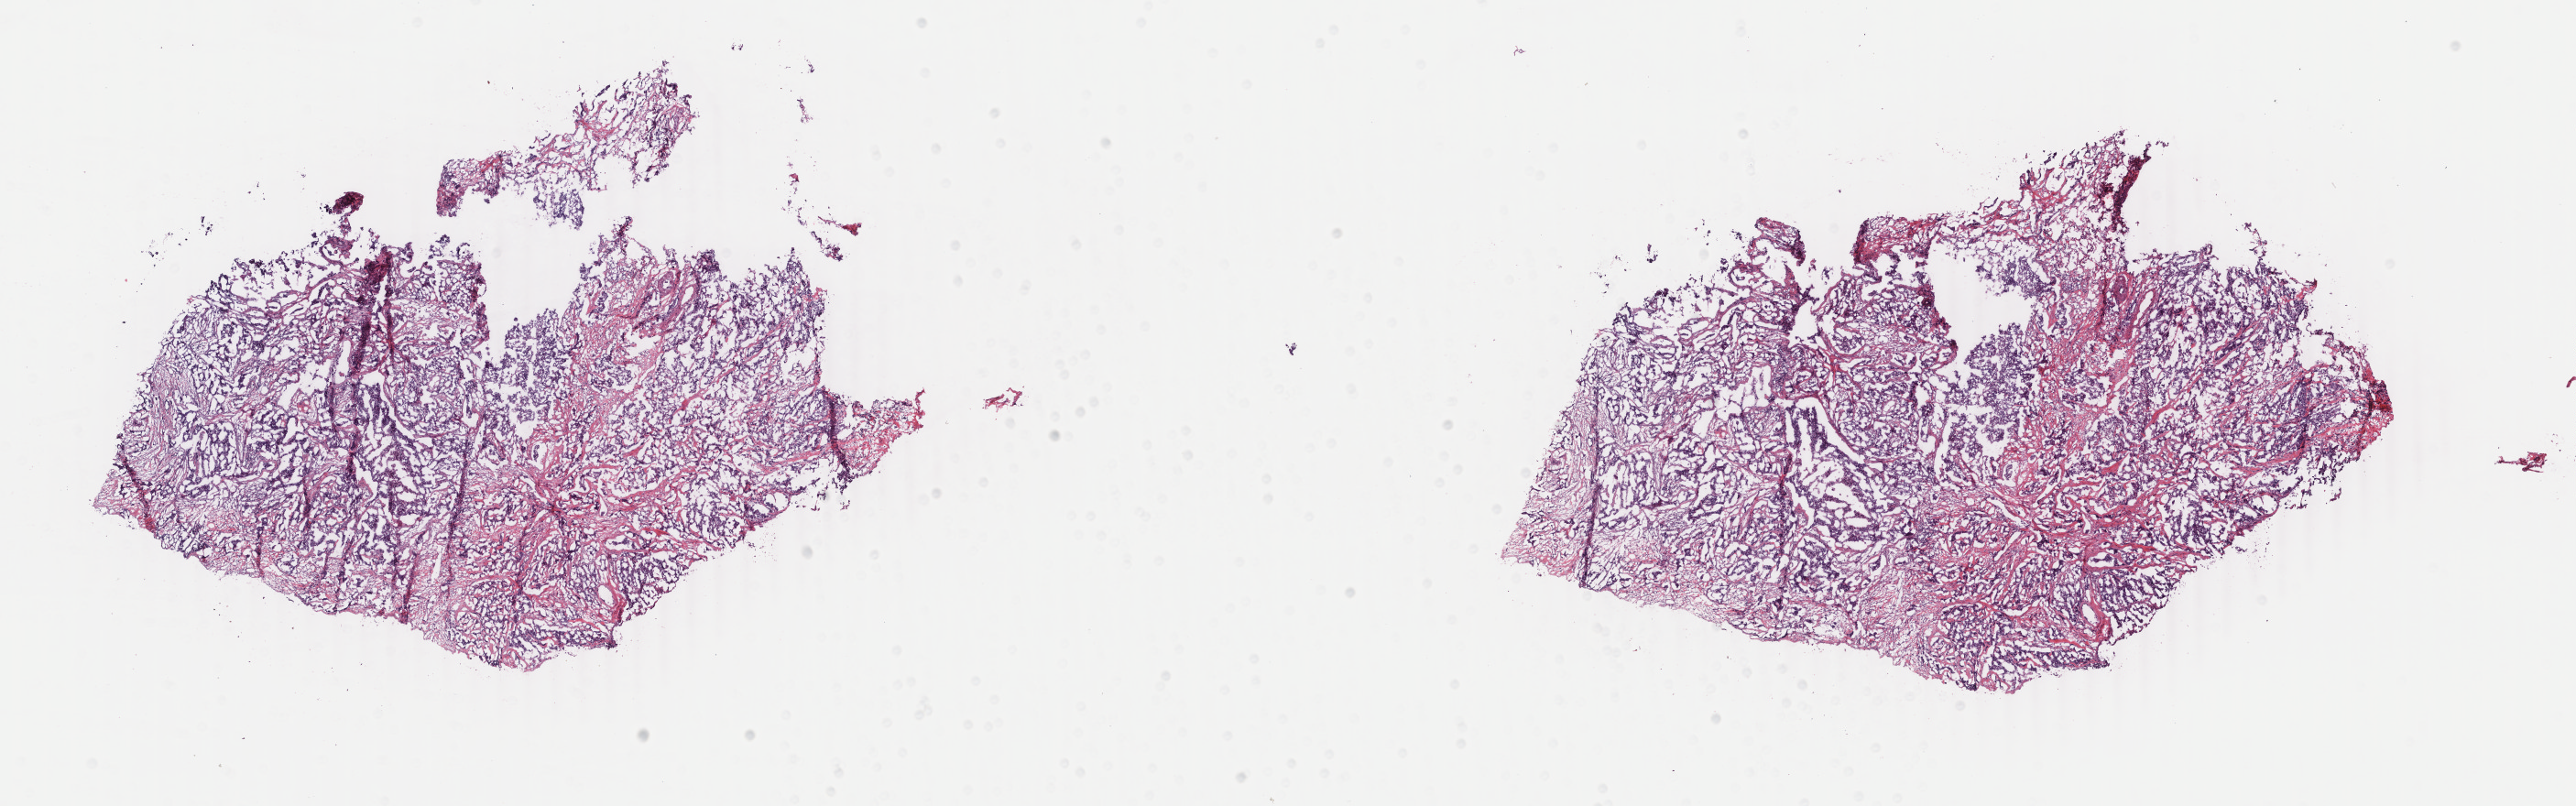
Whole-slide histology image, H&E-stained, low-resolution overview of the scanned area, about 22.4 x 7.0 mm (from a 40x scan); frozen section; sample: primary tumour, breast. Patient: female, age at initial diagnosis 61 years. Pathologist review of this section (percent, as recorded): tumour cells 80%, tumour nuclei 80%, normal cells 0%, stromal cells 20%, necrosis 0%. Inflammatory infiltration, as recorded: lymphocyte infiltration 0%, monocyte infiltration 0%, neutrophil infiltration 0%.
Laterality: right. Histologic diagnosis: Infiltrating duct carcinoma, NOS. Lymph nodes positive (case pathology): 0 of 14 examined.